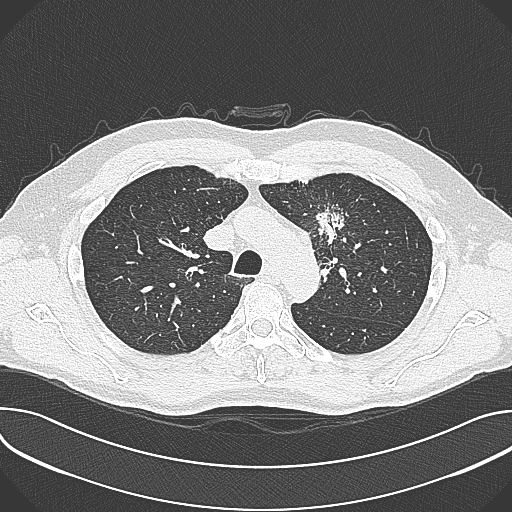
Low-dose screening chest CT, axial slice, baseline annual screen, lung window (W 1500 / L -600 HU), lung (sharp) reconstruction kernel (B80f), slice 92 of 361 in the series, 512 × 512 image matrix. Male, age 59 years at enrolment.
Lesion marked by an expert reader, bounding box [x1, y1, x2, y2] px = [302, 200, 359, 258]. The screening reader recorded 2 non-calcified nodules or masses ≥4 mm on this exam (left upper lobe, left upper lobe); which of them this box marks is not recorded. Lung cancer was diagnosed 21 days after this screen: non-small cell carcinoma, left upper lobe, poorly differentiated (G3), stage IIIA (AJCC 6th edition), 35 mm at pathology.